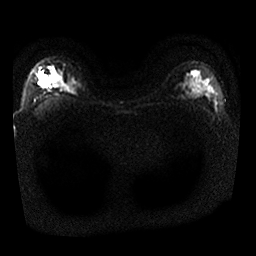
Breast MRI, one axial slice. Diffusion-weighted series; image 2 of 4 stored at this slice position (different b-values; order by instance number). 1.5 T. 4 mm slice thickness. 256 × 256 image matrix. Female patient.
Annotated regions visible in this slice (outlined manually by an expert reader):
- tumour on diffusion-weighted imaging: bounding box (x1, y1, x2, y2) in pixels: (40, 76, 50, 86)